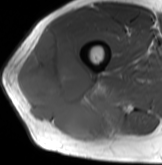
MRI of an extremity soft-tissue mass, one axial slice; position 49 of 61 along the scan axis; MR volume resampled by the dataset authors to the PET/CT grid (not the native acquisition matrix); 3.27 mm slice thickness; 162 × 165 image matrix, field of view 158 × 161 mm. Male patient. From the clinical record (not read from this slice): histological type: poorly differentiated synovial sarcoma; grade: high; site of the primary tumour: right buttock.
Structures marked on this image (expert contour drawn on MRI and transferred to this co-registered scan by the dataset authors):
- gross tumour volume including surrounding oedema: bounding box [x1, y1, x2, y2] px = [18, 29, 117, 140]
- gross tumour volume (mass): [18, 29, 117, 140]